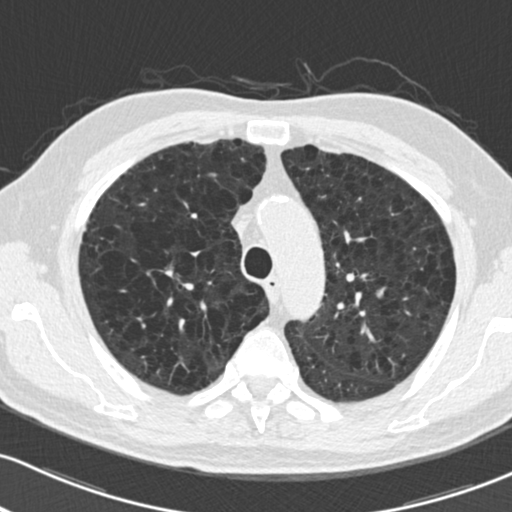
Low-dose screening chest CT, one axial slice; position 156 of 204 along the scan axis; reconstruction kernel B30f; 120 kVp; lung window (W 1500 / L -600 HU); 2 mm slice thickness; 512 × 512 image matrix.
Outlined on this slice (expert manual segmentation):
- lesion 1 (tumor, upper lobe of right lung): bounding box [x1, y1, x2, y2] px = [165, 267, 173, 277]